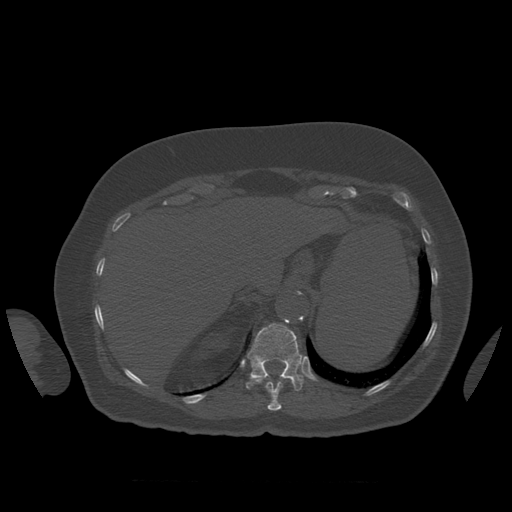
CT including the spine, one axial slice. Position 308 of 399 along the scan axis. Reconstruction kernel STANDARD. 120 kVp. Bone window (W 1800 / L 400 HU). 512 × 512 image matrix, field of view 404 × 404 mm. Patient age 81 years. From the clinical record (not read from this slice): primary cancer: renal.
Structures marked on this image (semi-automatic segmentation, software-assisted and operator-edited):
- T11 vertebra: bounding box <249,379,283,411> (left, top, right, bottom; pixels)
- T12 vertebra: <246,323,304,391>